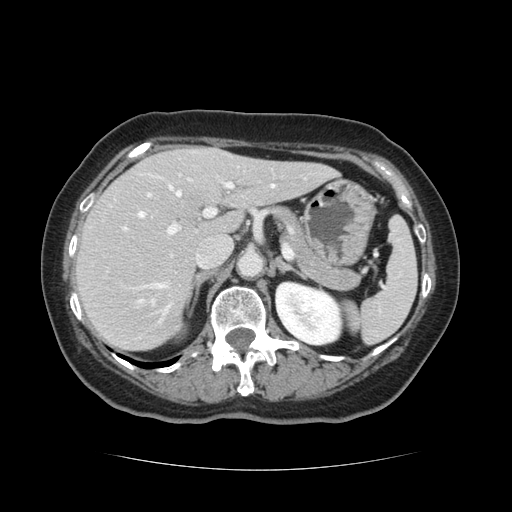
Contrast-enhanced abdominal CT, one axial slice. Slice 76 of 128 in the series (ordered by position). 120 kVp. Soft-tissue window (W 400 / L 40 HU). 512 × 512 image matrix, field of view 366 × 366 mm. Female patient, age 67 years. From the clinical record (not read from this slice): diagnosis: colorectal cancer liver metastases, imaged before liver resection; multiple liver metastases: yes; largest metastasis: 3 cm; disease in both lobes: yes.
Structures marked on this image (manually delineated by an expert):
- hepatic veins: box from (x=139, y=185) to (x=275, y=302) px
- liver: (x=74, y=146)–(x=333, y=351)
- planned liver remnant (the part of the liver to remain after resection): (x=75, y=159)–(x=333, y=350)
- portal vein (with intrahepatic branches): (x=122, y=174)–(x=234, y=305)